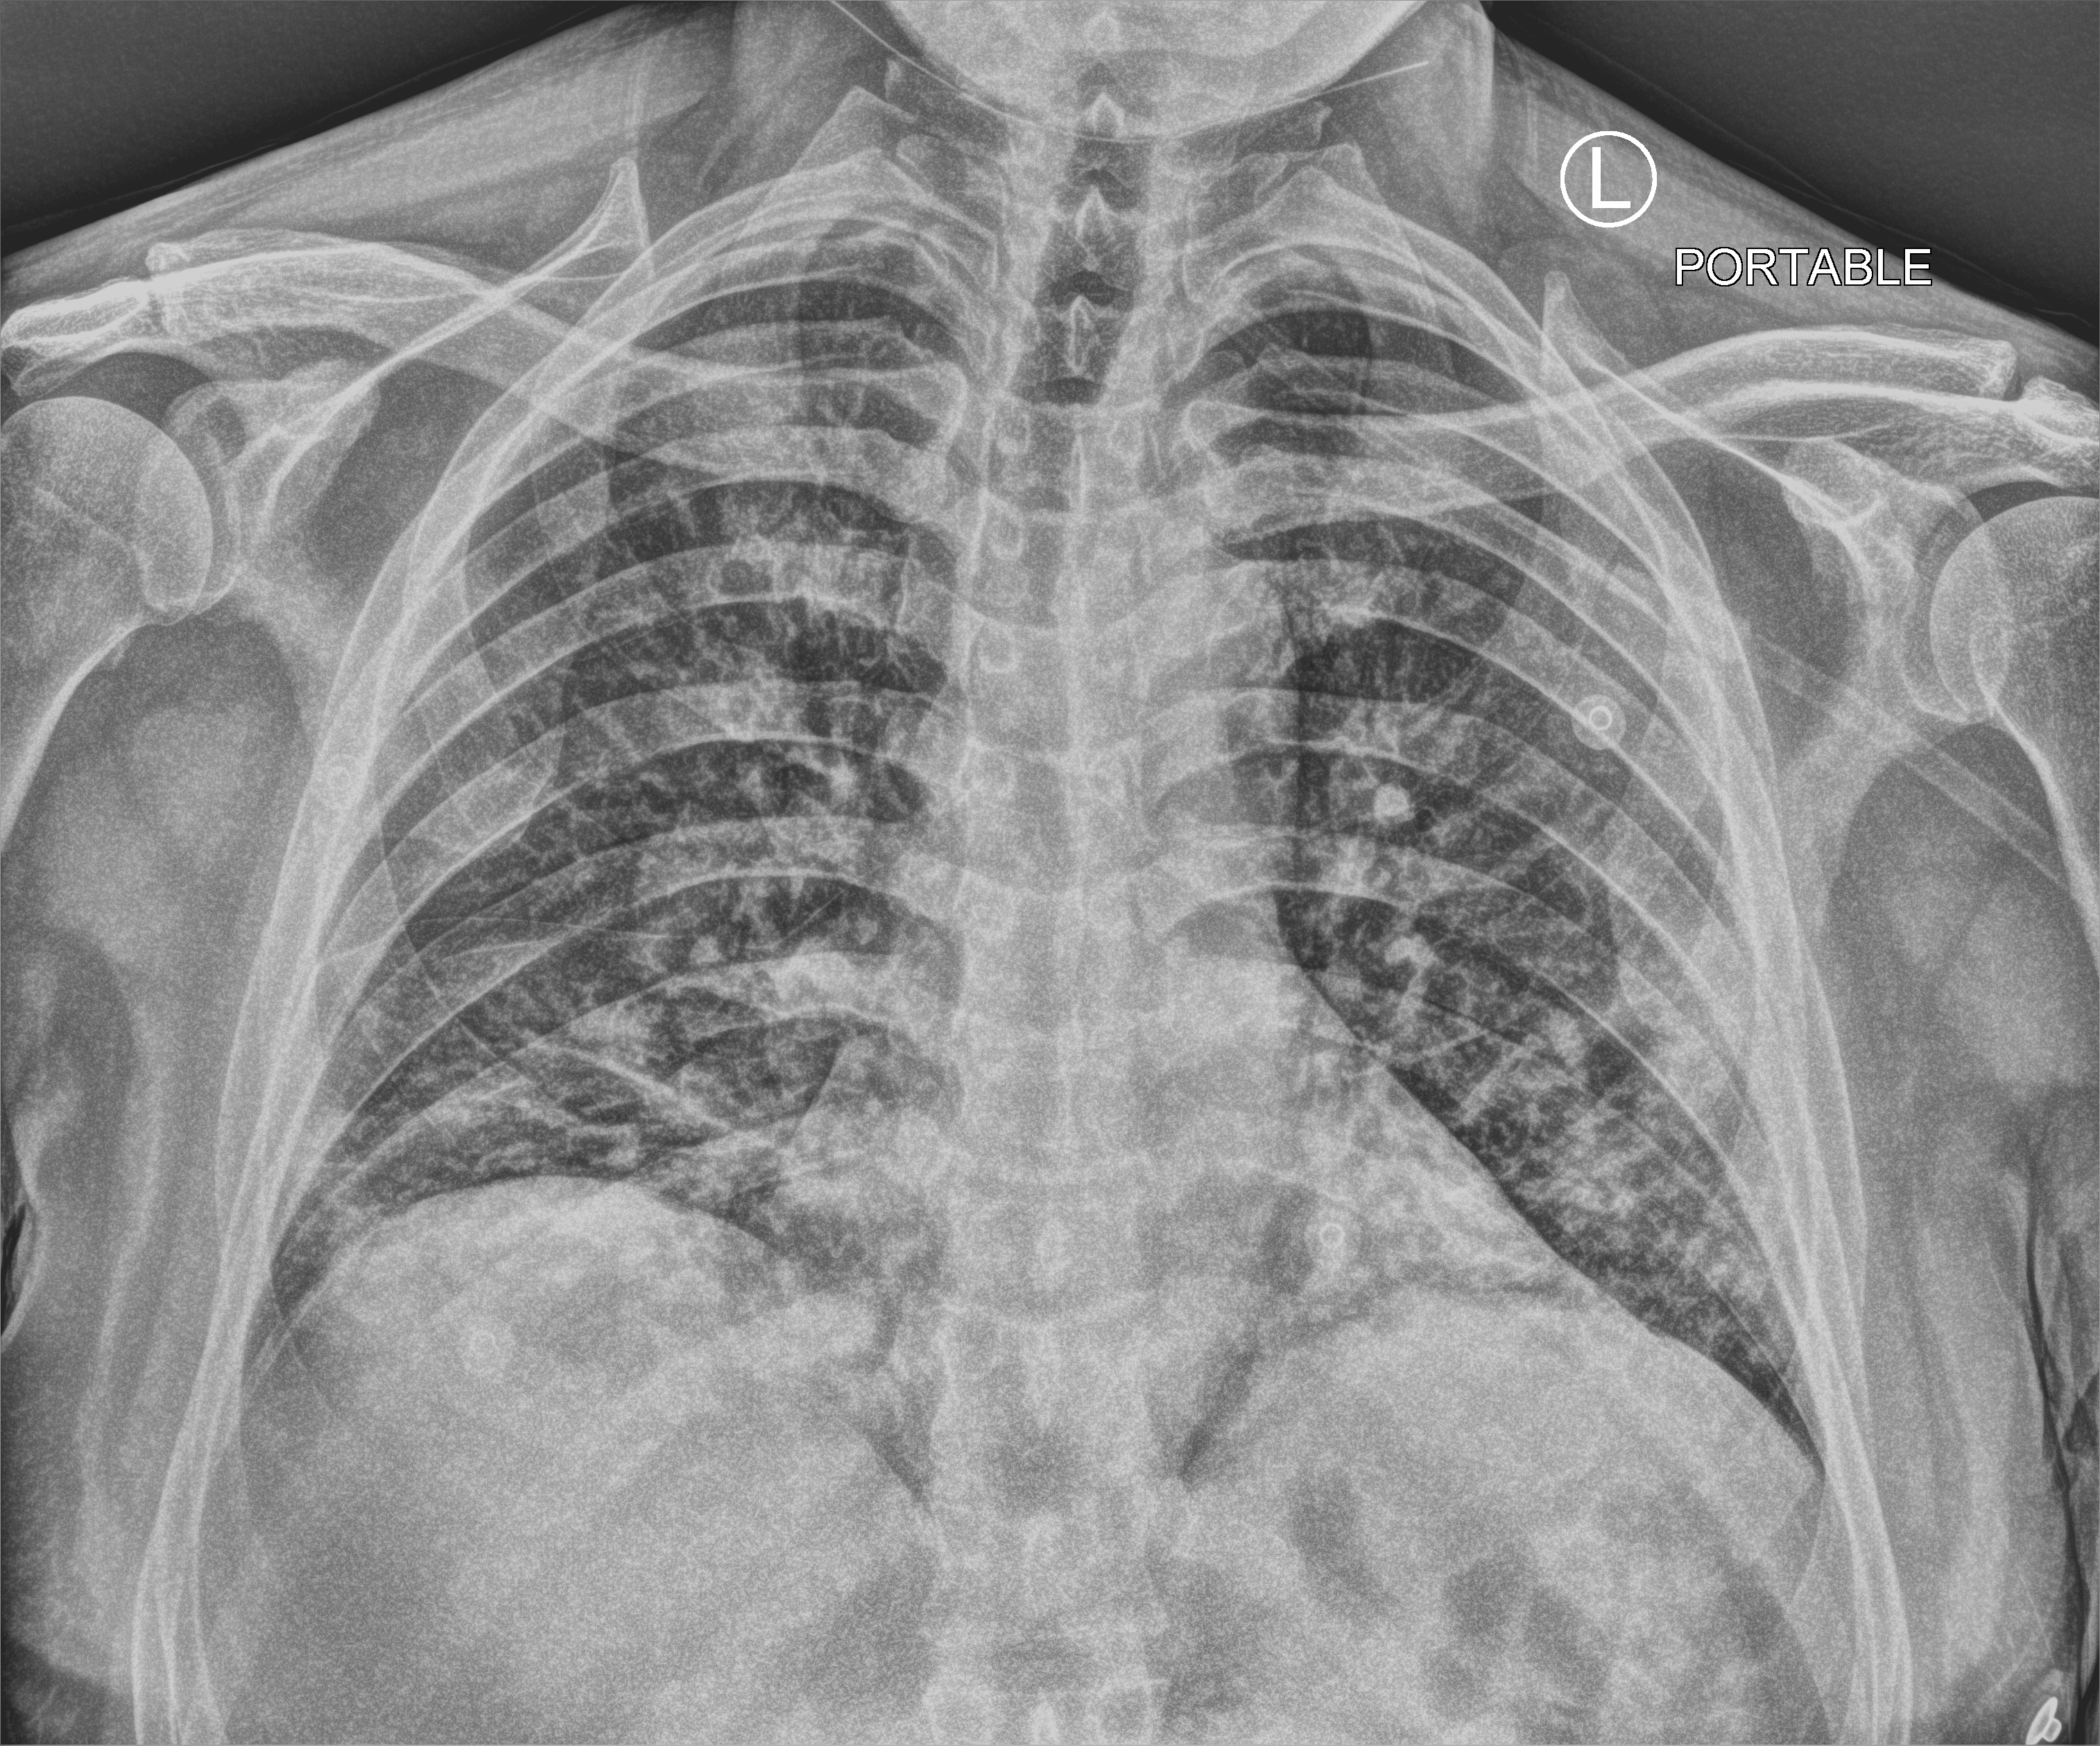
Chest X-ray (portable); anteroposterior (AP) projection. Patient hospitalised with COVID-19; male, aged 18–59 years.
From the hospital-stay record, not from the radiograph (when in the stay this image was taken is not recorded): mechanically ventilated during this hospital stay: no; length of hospital stay: 4 days.